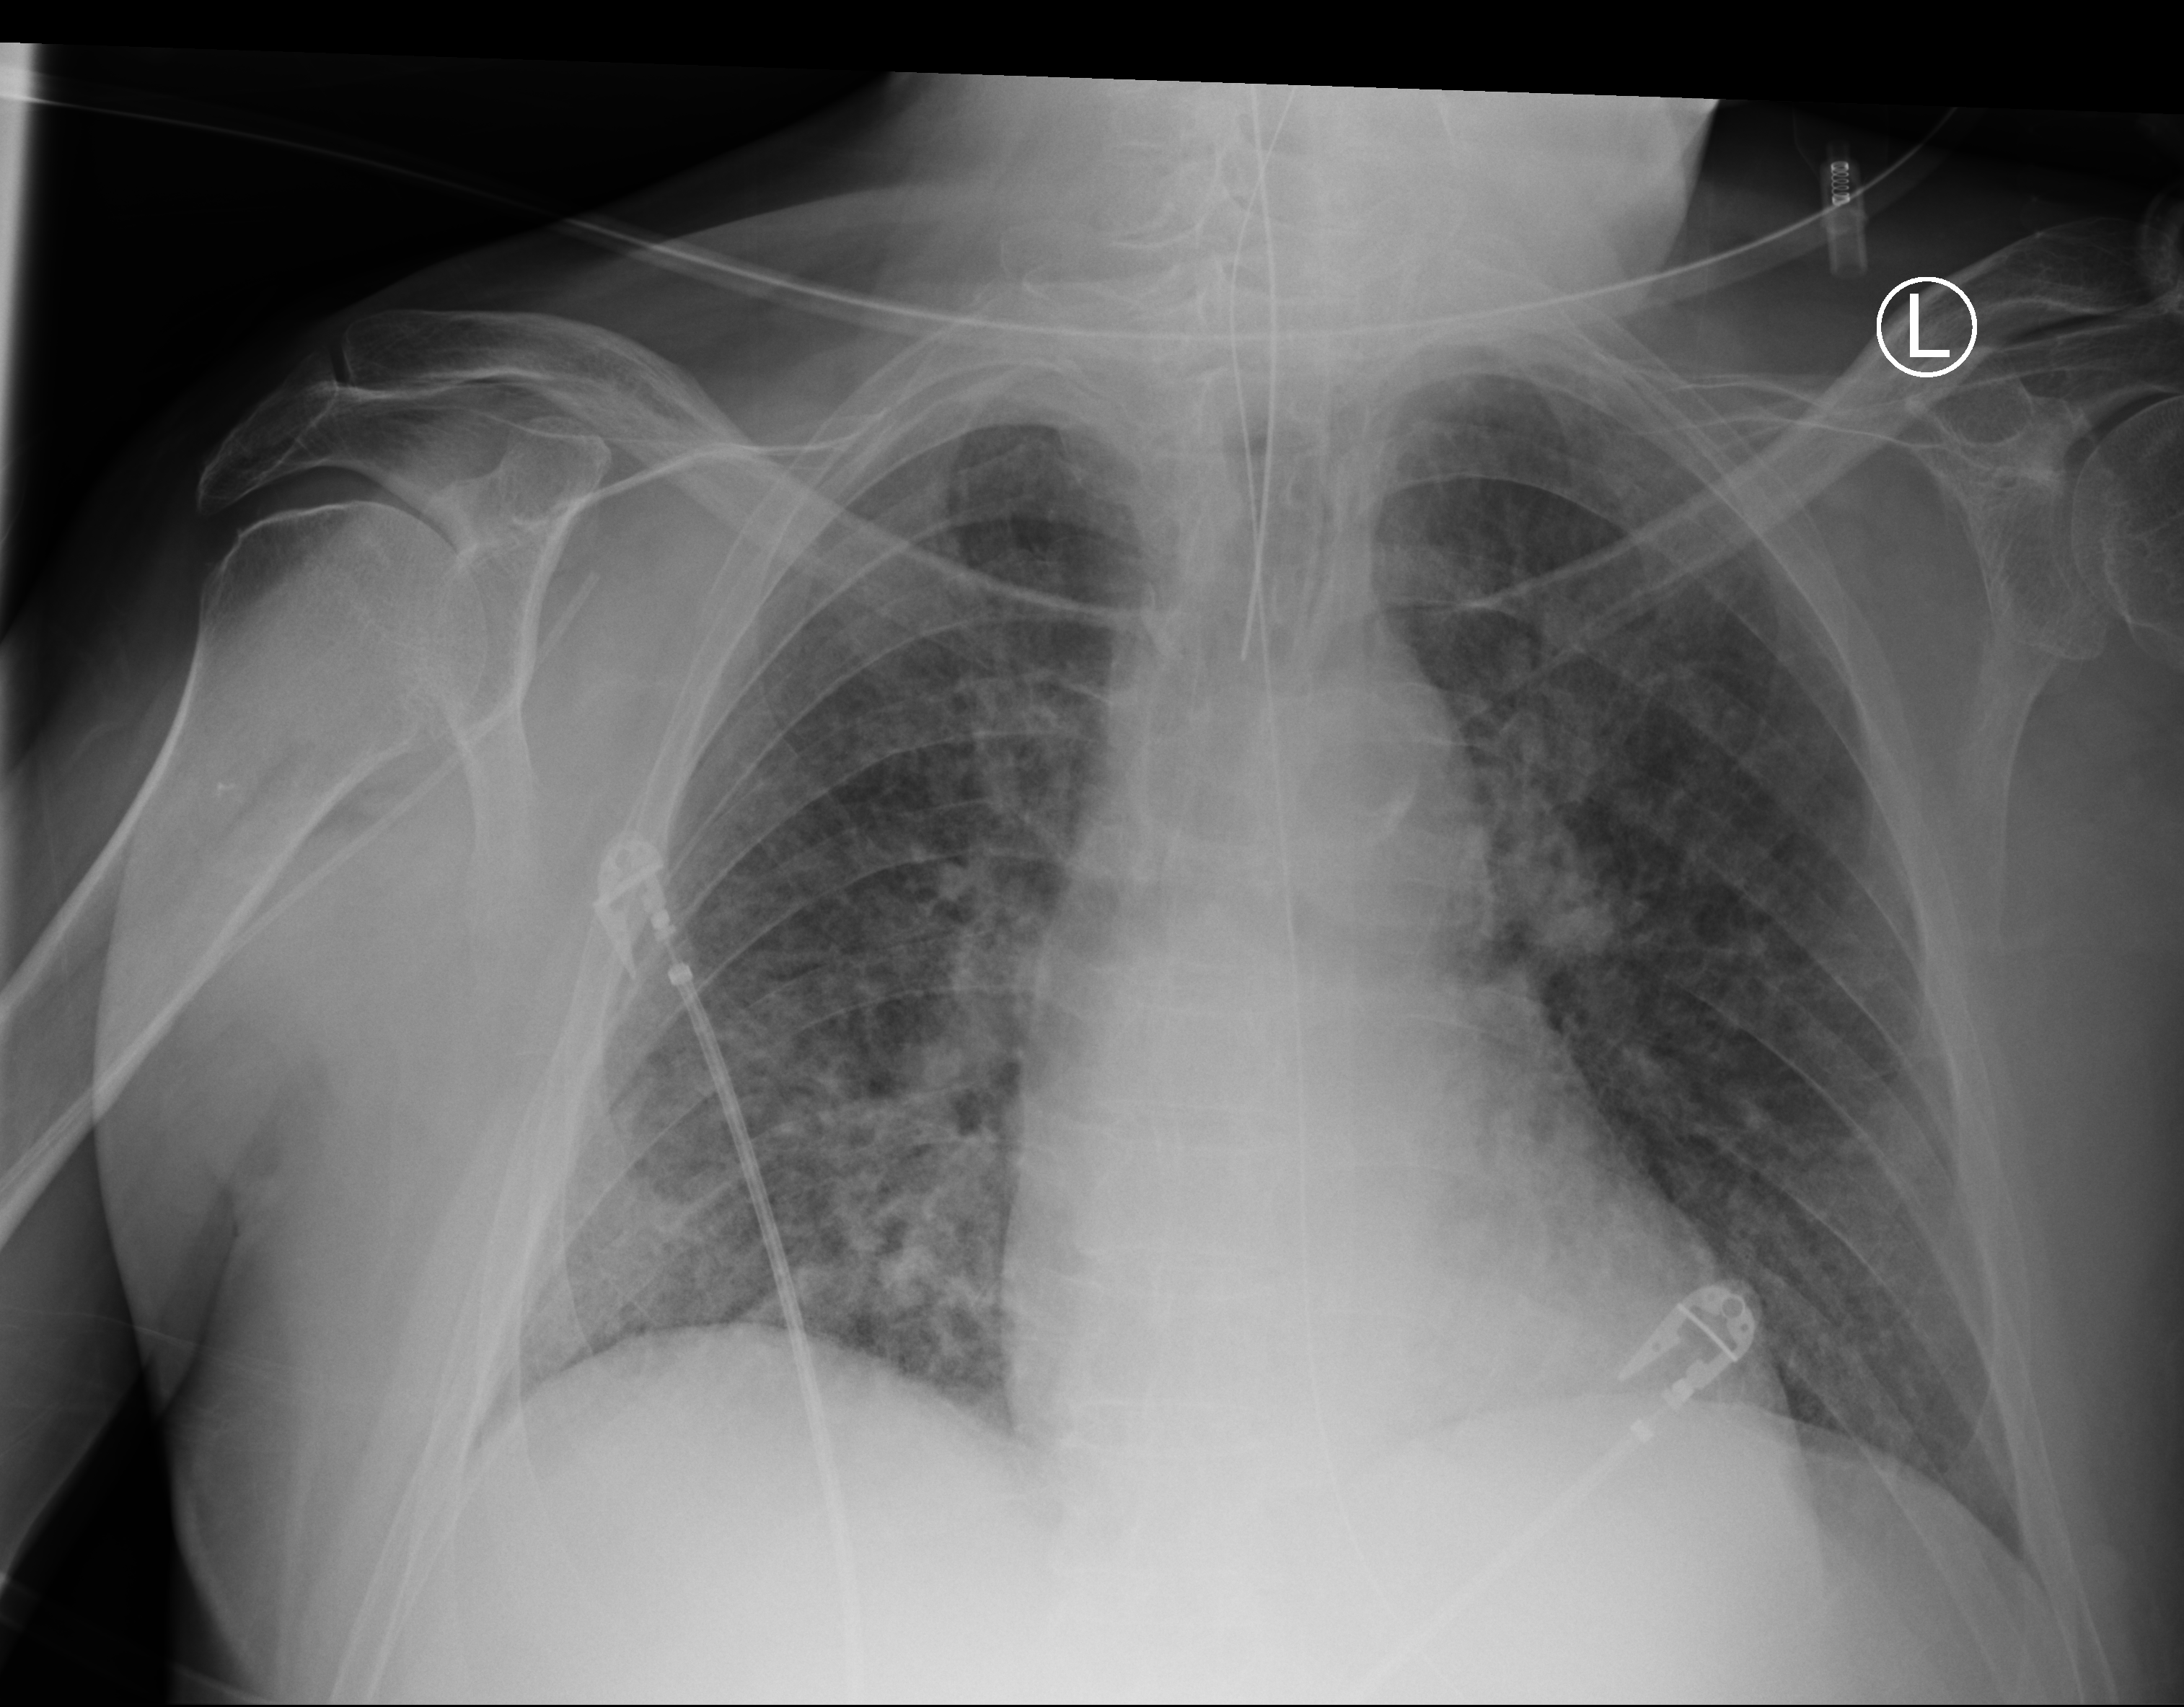
Portable chest radiograph, anteroposterior (AP) projection. Patient hospitalised with COVID-19; male, aged 60–74 years.
Hospital-stay facts (about this admission, not read from this image; timing relative to this image not recorded): admitted to intensive care during this hospital stay: yes; length of hospital stay: 25 days.